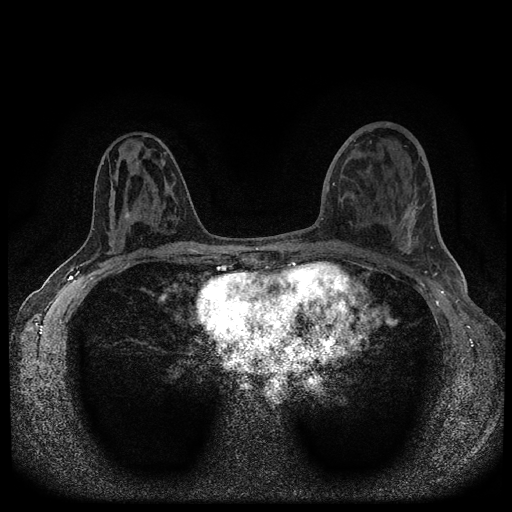
Breast MRI (dynamic contrast-enhanced, multi-phase), one axial slice; position 56 of 116 along the scan axis; dynamic contrast-enhanced series, time point 2 of 5 at this slice position (early post-contrast); 1.5 T; TE 2.7 ms, TR 5.6 ms; 512 × 512 image matrix, field of view 310 × 310 mm. Patient: female, 40 years.
Annotated regions visible in this slice (semi-automatic segmentation, software-assisted and operator-edited):
- breast lesion (labelled benign in the annotation): bounding box (x1, y1, x2, y2) in pixels: (123, 202, 131, 221)